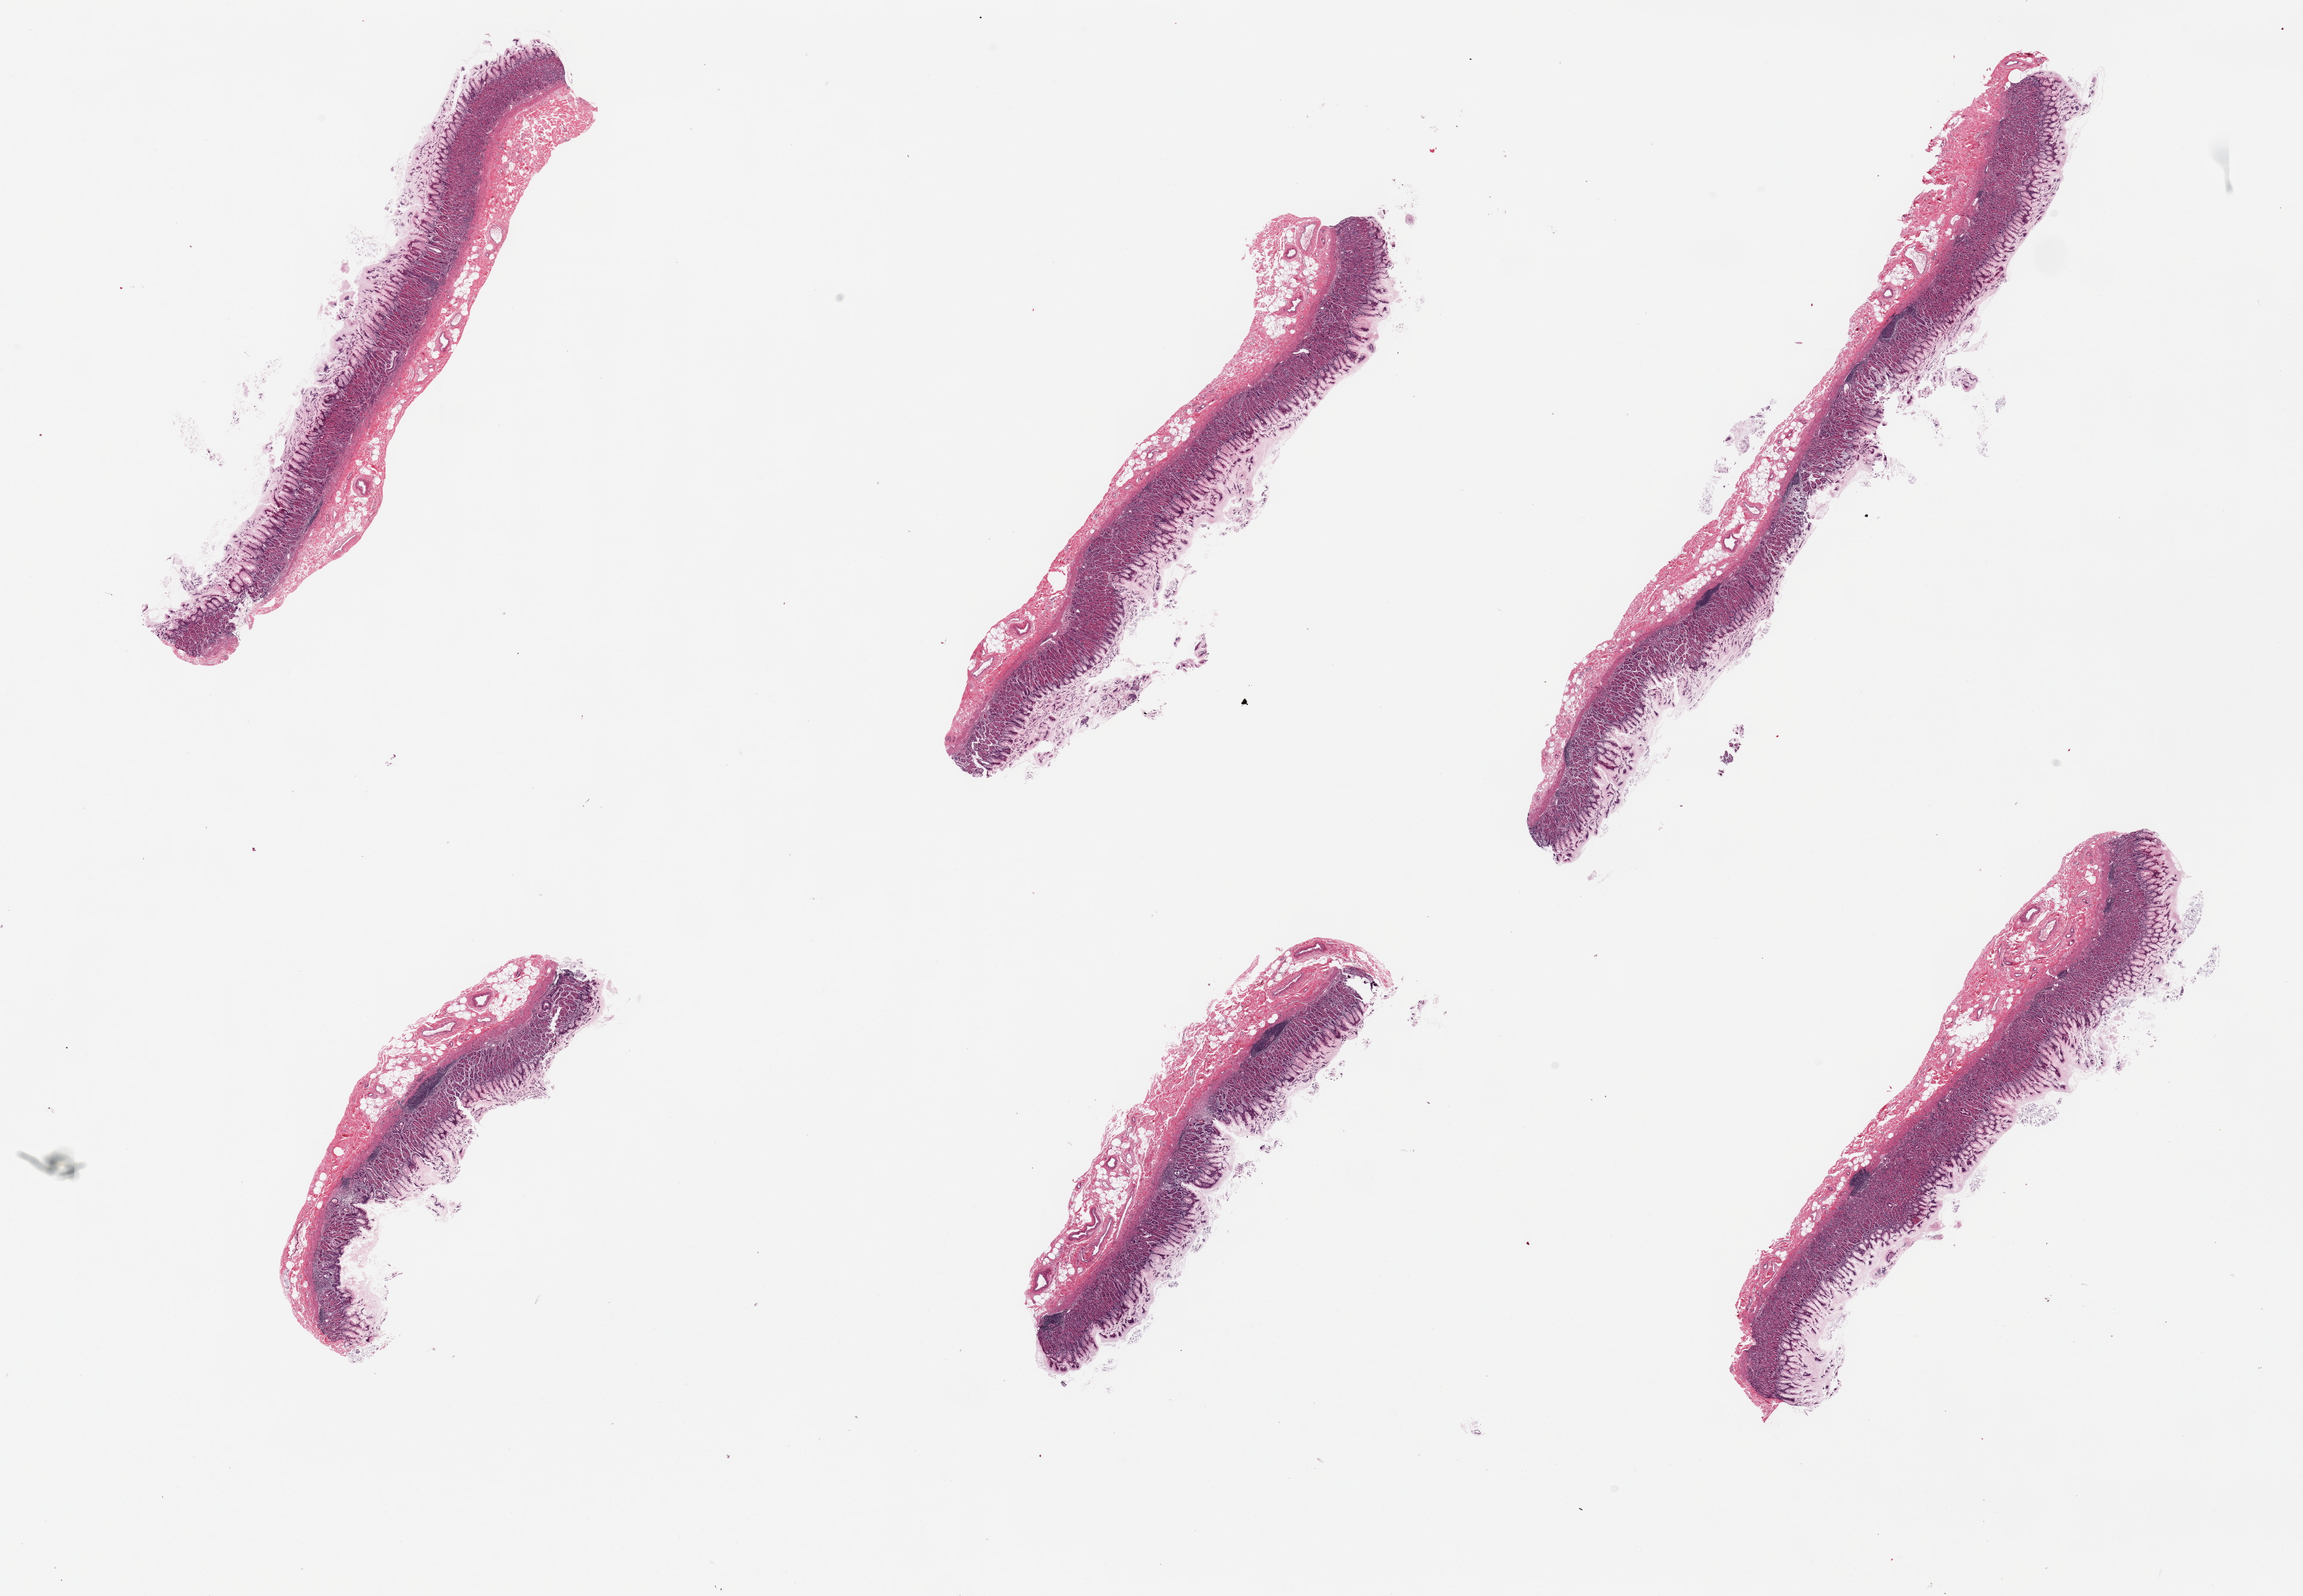
H&E whole-slide image, brightfield — a low-resolution overview of the entire scanned area, about 30.5 x 21.1 mm (from a 20x scan); PAXgene-fixed paraffin-embedded (PFPE) section; sampled site (target tissue): stomach; tissue donor sample. Donor: female.
Review note (as recorded): 6 pieces. Mucosa and submucosa; sloughing of superficial (foveolar) glands.